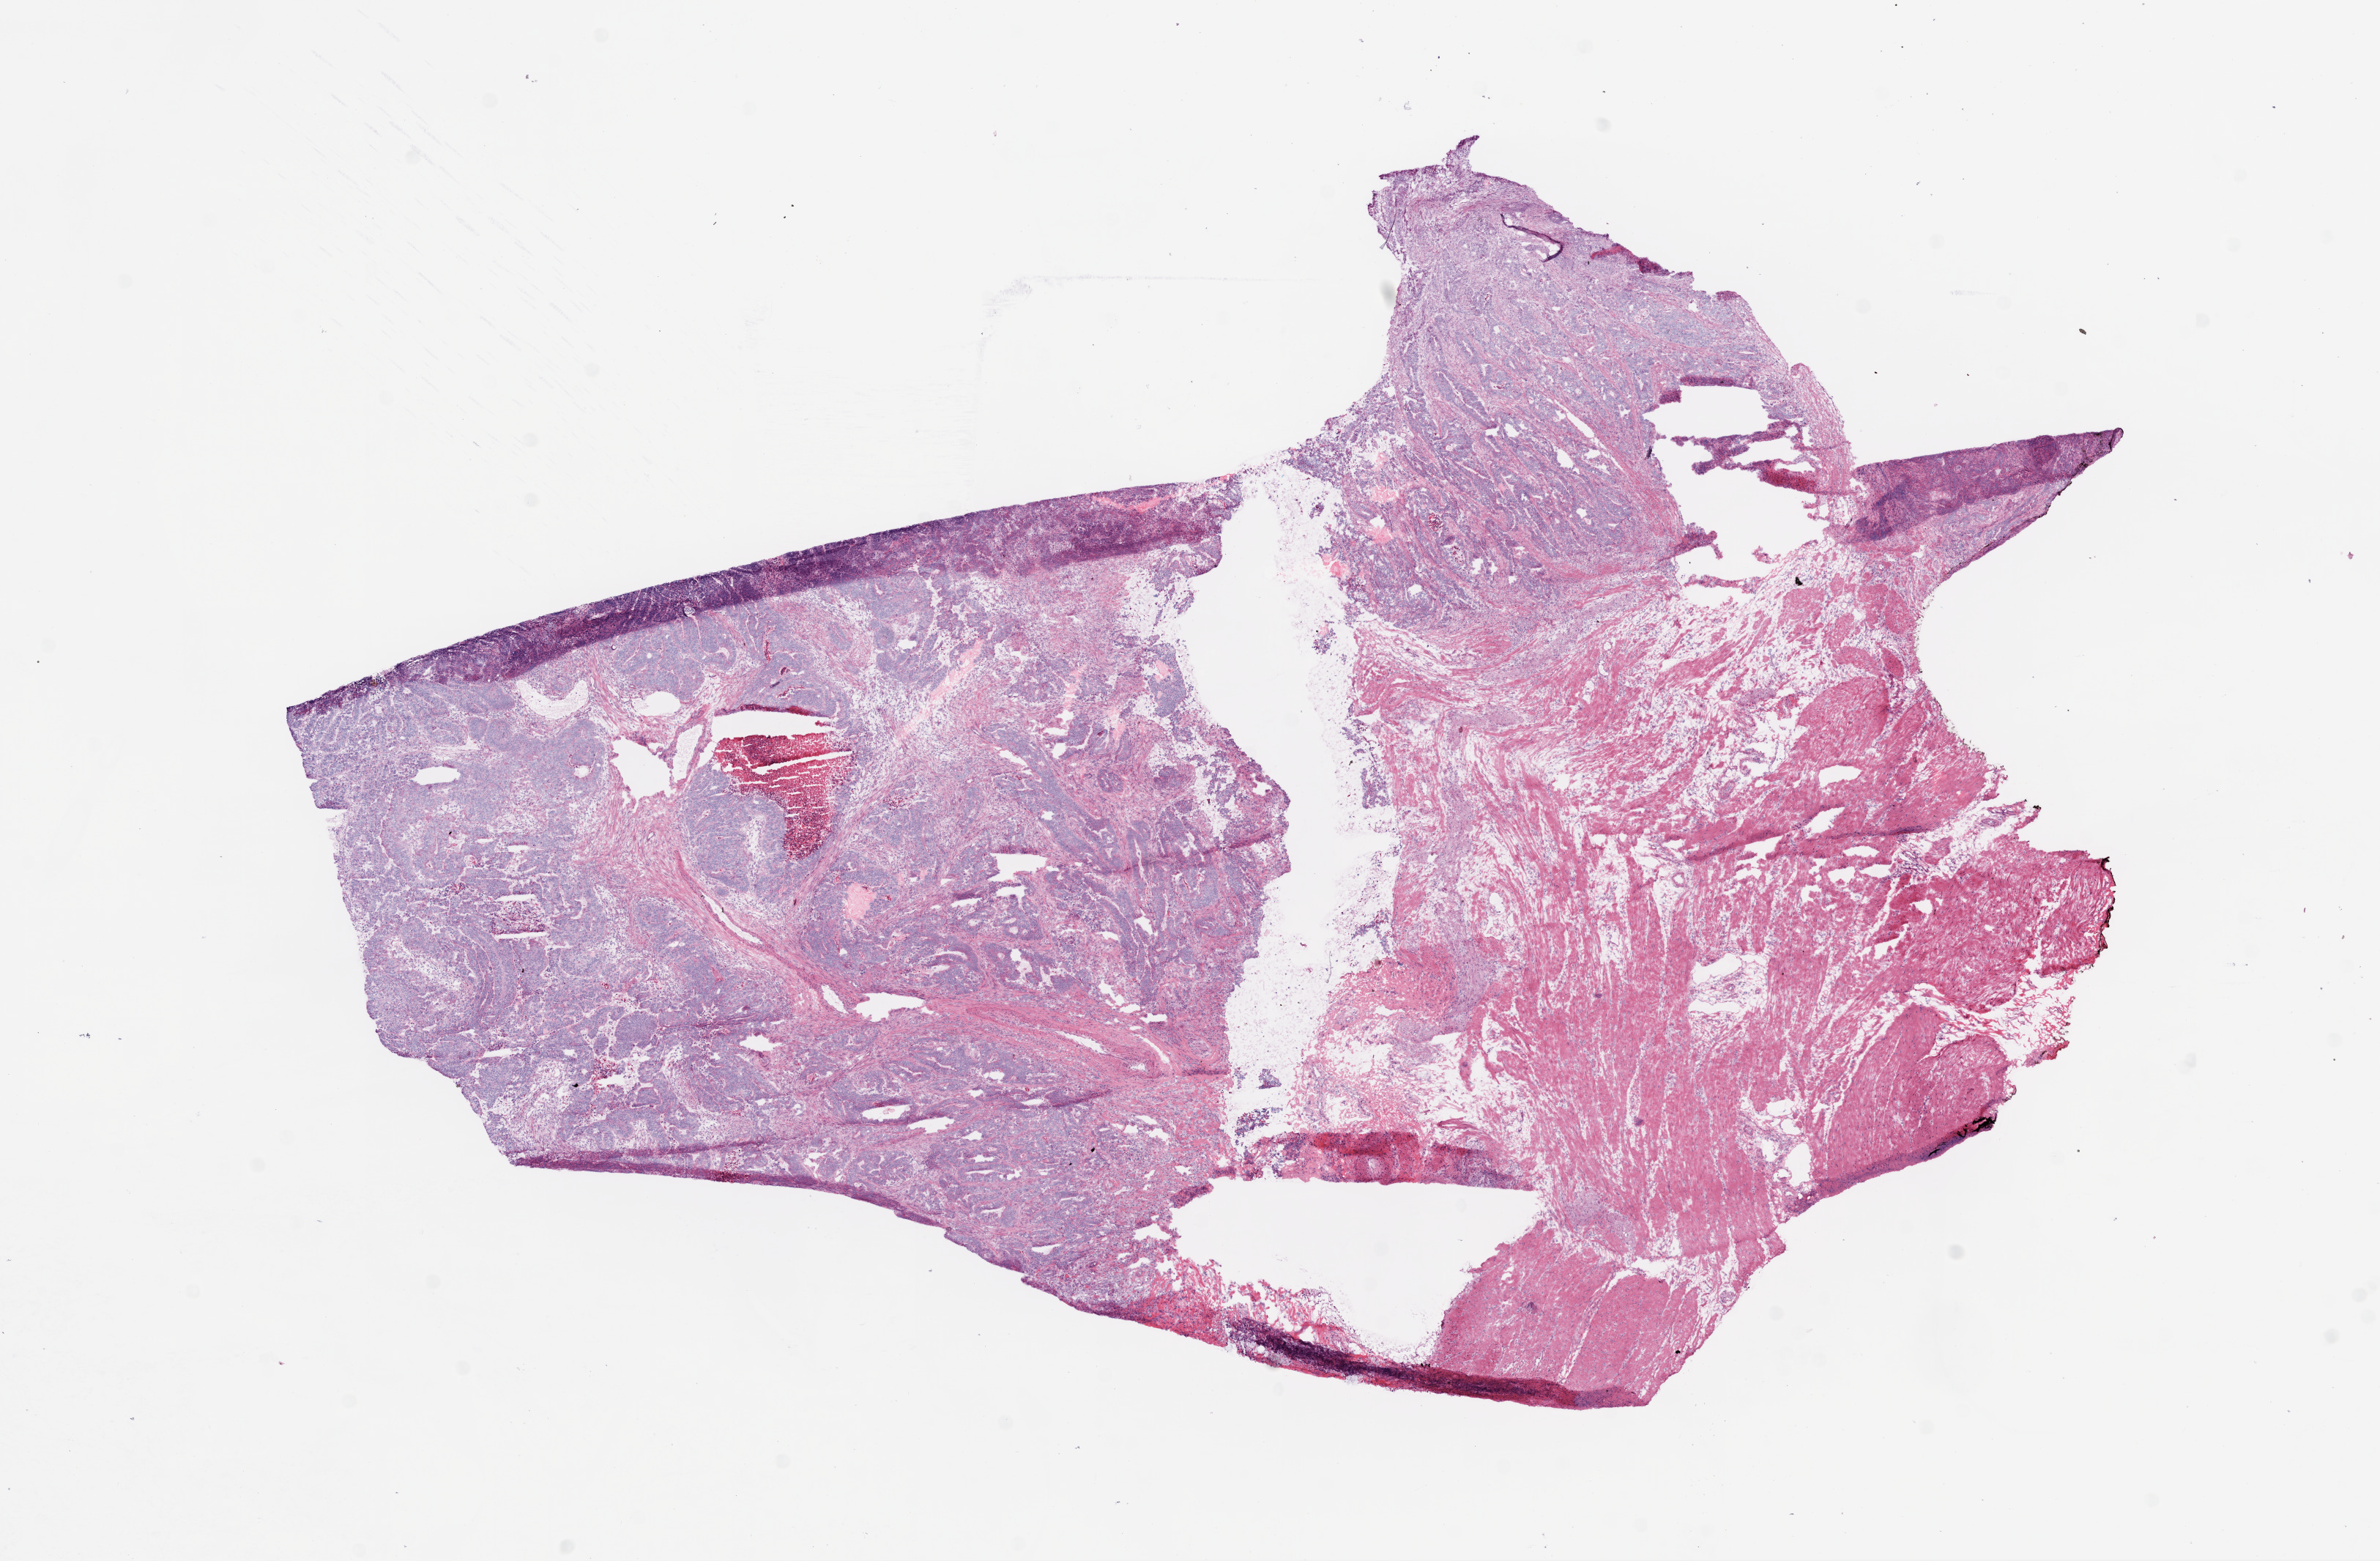
H&E whole-slide image, low-resolution overview of the scanned area, about 13.0 x 8.5 mm (slide scanned at 20x), frozen section from the top of the tissue portion, primary tumour sample from the rectum. Patient: male, age at initial diagnosis 48 years. Composition of this section per pathologist review: tumour cells 55%, tumour nuclei 75%, normal cells 30%, stromal cells 10%, necrosis 5%.
Lymph nodes positive (case pathology): 9 of 18 examined. AJCC pathologic stage: IIIC. Histologic diagnosis: Adenocarcinoma, NOS.